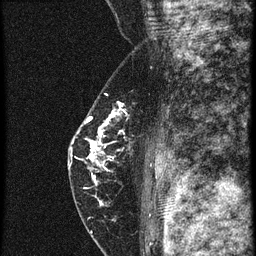
Breast MRI (dynamic contrast-enhanced), one sagittal slice; 4 images stored at this slice position (order not interpretable as contrast timing); 1.5 T; TE 4.2 ms, TR 20.4 ms; 1.5 mm slice thickness; 256 × 256 image matrix, field of view 180 × 180 mm. Patient: female, 46 years. From the clinical record (not read from this slice): setting: breast cancer imaged before/during neoadjuvant chemotherapy; receptor status: triple-negative.
Annotated regions visible in this slice (semi-automatic segmentation, software-assisted and operator-edited):
- analysis volume of interest (the breast-tissue region the enhancement analysis was run in; not a lesion): box from (x=67, y=82) to (x=155, y=201) px
- tumour enhancement mask (voxels above the 90 % enhancement threshold inside the analysis volume of interest): (x=71, y=112)–(x=122, y=187)